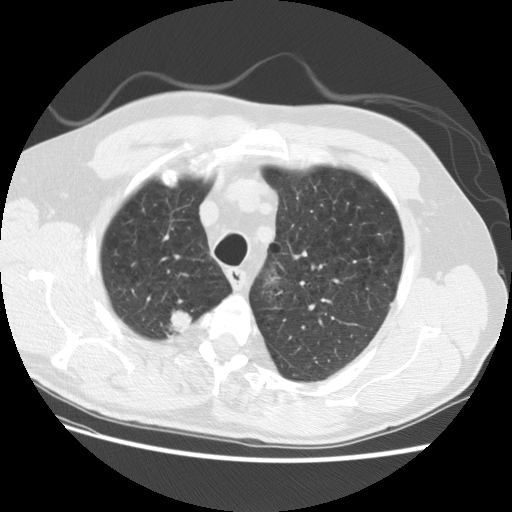
Low-dose screening chest CT, one axial slice. Position 101 of 124 along the scan axis. Reconstruction kernel STANDARD. 140 kVp. Lung window (W 1500 / L -600 HU). 2.5 mm slice thickness. 512 × 512 image matrix.
Outlined on this slice (outlined manually by an expert reader):
- lesion 1 (tumor, upper lobe of right lung): box from (x=169, y=302) to (x=193, y=333) px